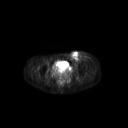
FDG PET of an extremity soft-tissue mass (from a PET/CT study), one axial slice; slice 73 of 267 in the series (ordered by position); 128 × 128 image matrix. Female patient, age 24 years. From the clinical record (not read from this slice): histological type: leiomyosarcoma; grade: high; site of the primary tumour: groin.
Outlined on this slice (expert contour drawn on MRI and transferred to this co-registered scan by the dataset authors):
- gross tumour volume including surrounding oedema: bounding box <68,51,92,65> (left, top, right, bottom; pixels)
- gross tumour volume (mass): <69,51,82,64>